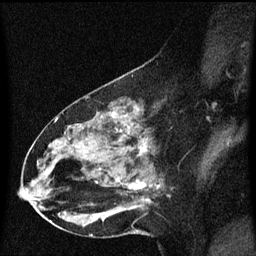
Breast MRI (dynamic contrast-enhanced), one sagittal slice. Position 33 of 60 along the scan axis. Dynamic contrast-enhanced series, image 2 of 3 at this slice position (ordered by acquisition). 1.5 T. TE 4.2 ms, TR 8.4 ms. 2 mm slice thickness. 256 × 256 image matrix, field of view 200 × 200 mm. Female patient, age 49 years. Case-level facts recorded for this patient, not image findings: setting: breast cancer imaged before/during neoadjuvant chemotherapy; receptor status: HR-positive, HER2-negative.
Outlined on this slice (semi-automatically segmented with operator editing):
- analysis volume of interest (the breast-tissue region the enhancement analysis was run in; not a lesion): bounding box <27,96,170,221> (left, top, right, bottom; pixels)
- tumour enhancement mask (voxels above the 70 % enhancement threshold inside the analysis volume of interest): <122,130,147,155>